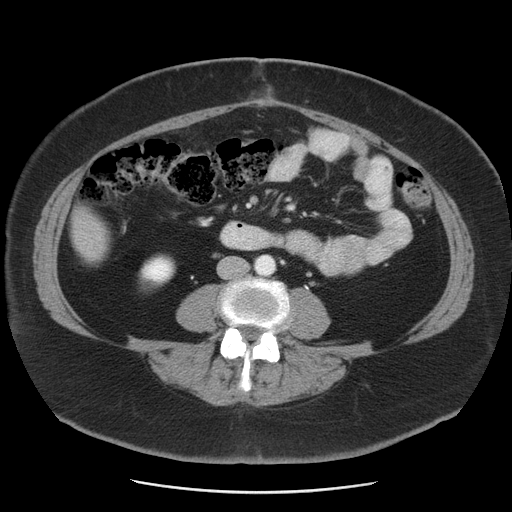
Contrast-enhanced abdominal CT, one axial slice; reconstruction kernel STANDARD; 120 kVp; intravenous contrast given; soft-tissue window (W 400 / L 40 HU); 512 × 512 image matrix, field of view 380 × 380 mm. Female patient, age 52 years. Case-level facts recorded for this patient, not image findings: diagnosis: colorectal cancer liver metastases, imaged before liver resection; multiple liver metastases: yes; largest metastasis: 2.5 cm; chemotherapy before resection: no.
Structures marked on this image (expert manual segmentation):
- liver: box from (x=71, y=208) to (x=110, y=264) px
- planned liver remnant (the part of the liver to remain after resection): (x=71, y=209)–(x=110, y=264)